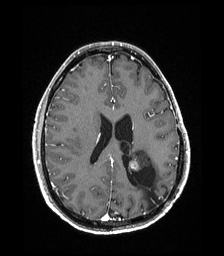
Brain MRI from a brain-tumour surgery series, one axial slice; slice 79 of 192 in the series (ordered by position); T1-weighted post-contrast; 1 mm slice thickness; 224 × 256 image matrix, field of view 224 × 256 mm. From the clinical record (not read from this slice): histopathology: Low grade glioma; IDH mutation: no.
Structures marked on this image (outlined manually by an expert reader):
- previous resection cavity: bounding box (x1, y1, x2, y2) in pixels: (127, 166, 162, 208)
- tumour: (128, 149, 151, 171)